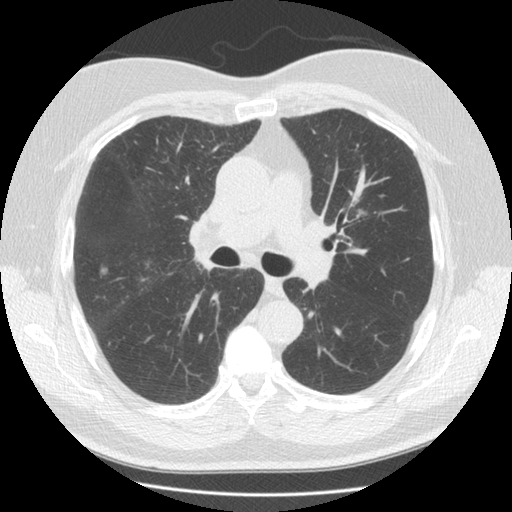
Low-dose screening chest CT, one axial slice; position 87 of 146 along the scan axis; lung window (W 1500 / L -600 HU); 2.5 mm slice thickness; 512 × 512 image matrix.
Structures marked on this image (outlined manually by an expert reader):
- lesion 1 (tumor, upper lobe of right lung): bounding box (x1, y1, x2, y2) in pixels: (99, 264, 110, 279)